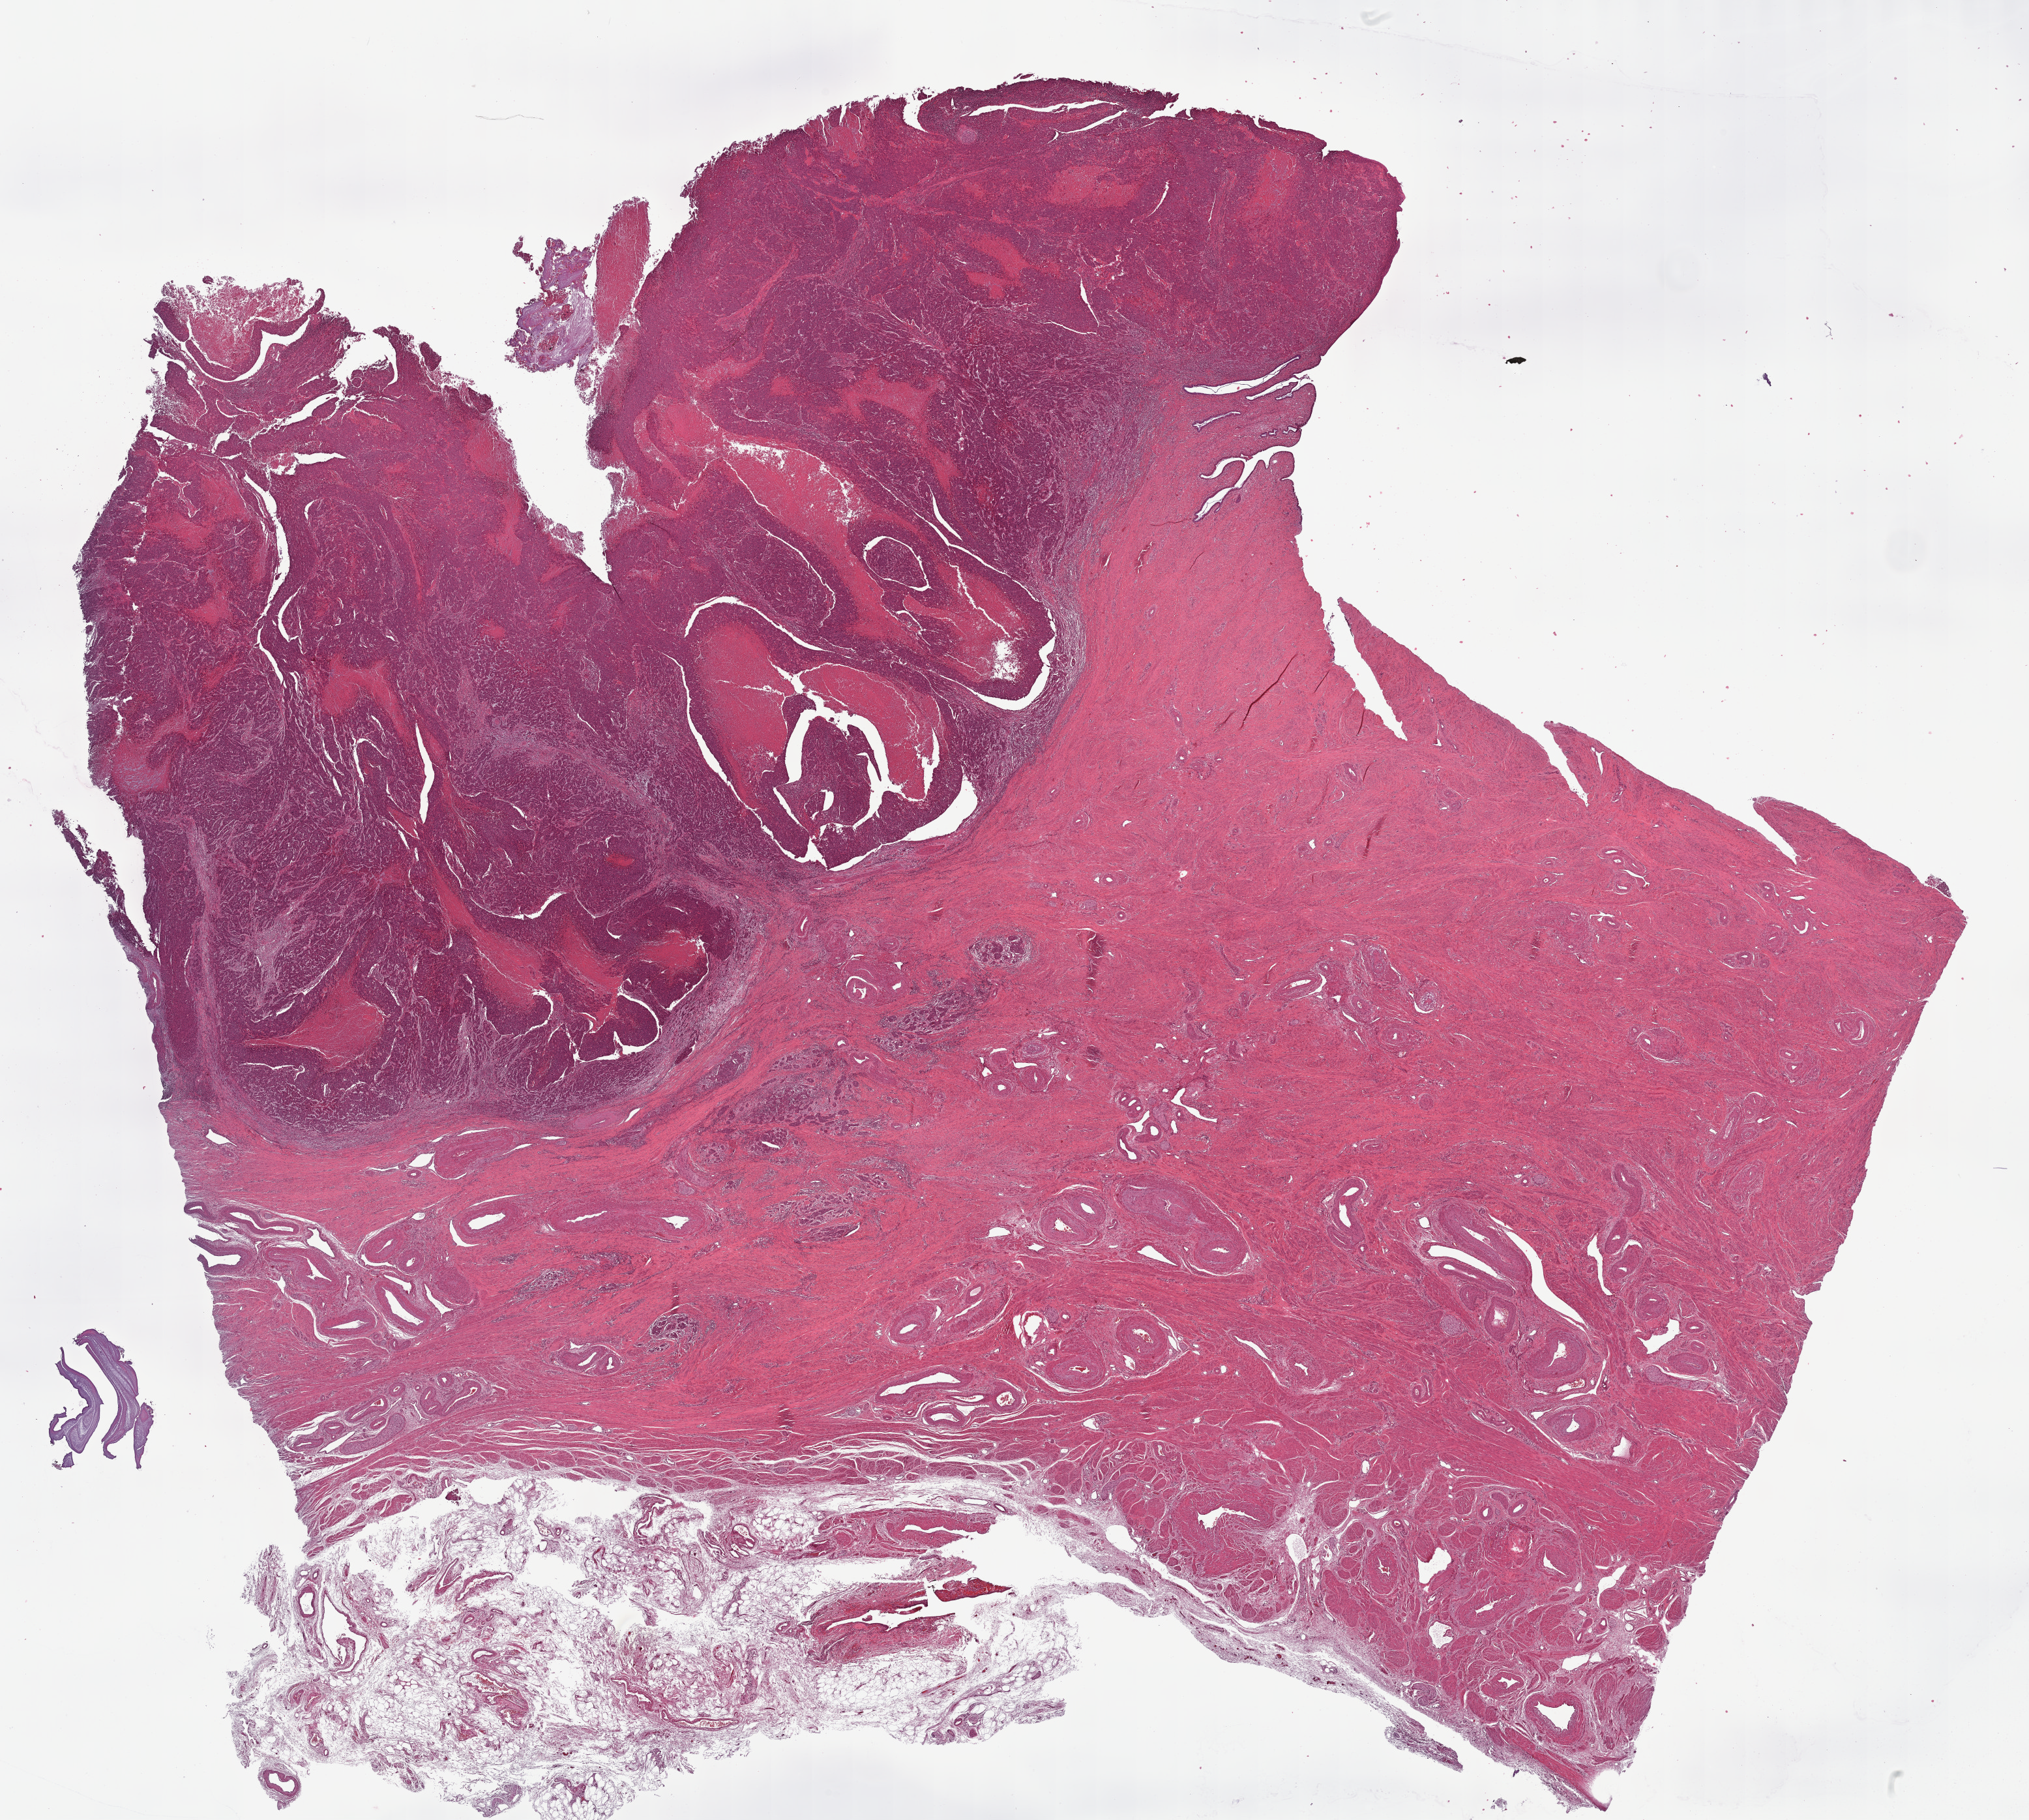
Digitized H&E tissue section (whole slide), whole scanned area (about 25.1 x 22.6 mm, slide scanned at 40x) shown as a low-resolution overview; FFPE section; primary tumour sample from the cervix. Female patient; age at initial diagnosis 42 years. Histologic grade: G3 (poorly differentiated).
Lymph nodes positive (case pathology): 0 of 24 examined. FIGO stage: IB1. Diagnosis: Squamous cell carcinoma, large cell, nonkeratinizing, NOS (cervix uteri).